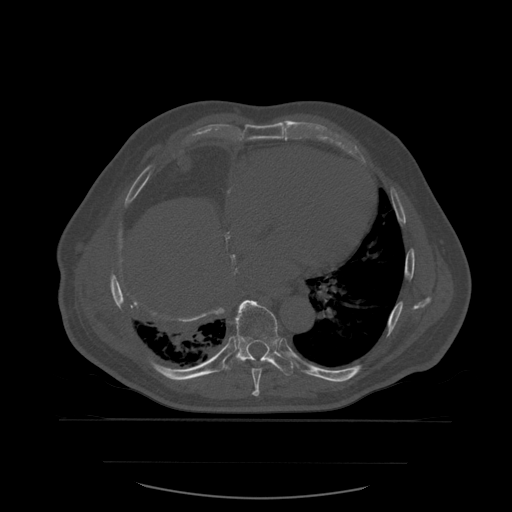
CT including the spine, one axial slice; position 348 of 590 along the scan axis; bone window (W 1800 / L 400 HU); 1.25 mm slice thickness; 512 × 512 image matrix, field of view 479 × 479 mm. Patient age 71 years. Case-level facts recorded for this patient, not image findings: primary cancer: lung.
Annotated regions visible in this slice (semi-automatically segmented with operator editing):
- T8 vertebra: bounding box <252,368,262,397> (left, top, right, bottom; pixels)
- T9 vertebra: <221,300,294,376>